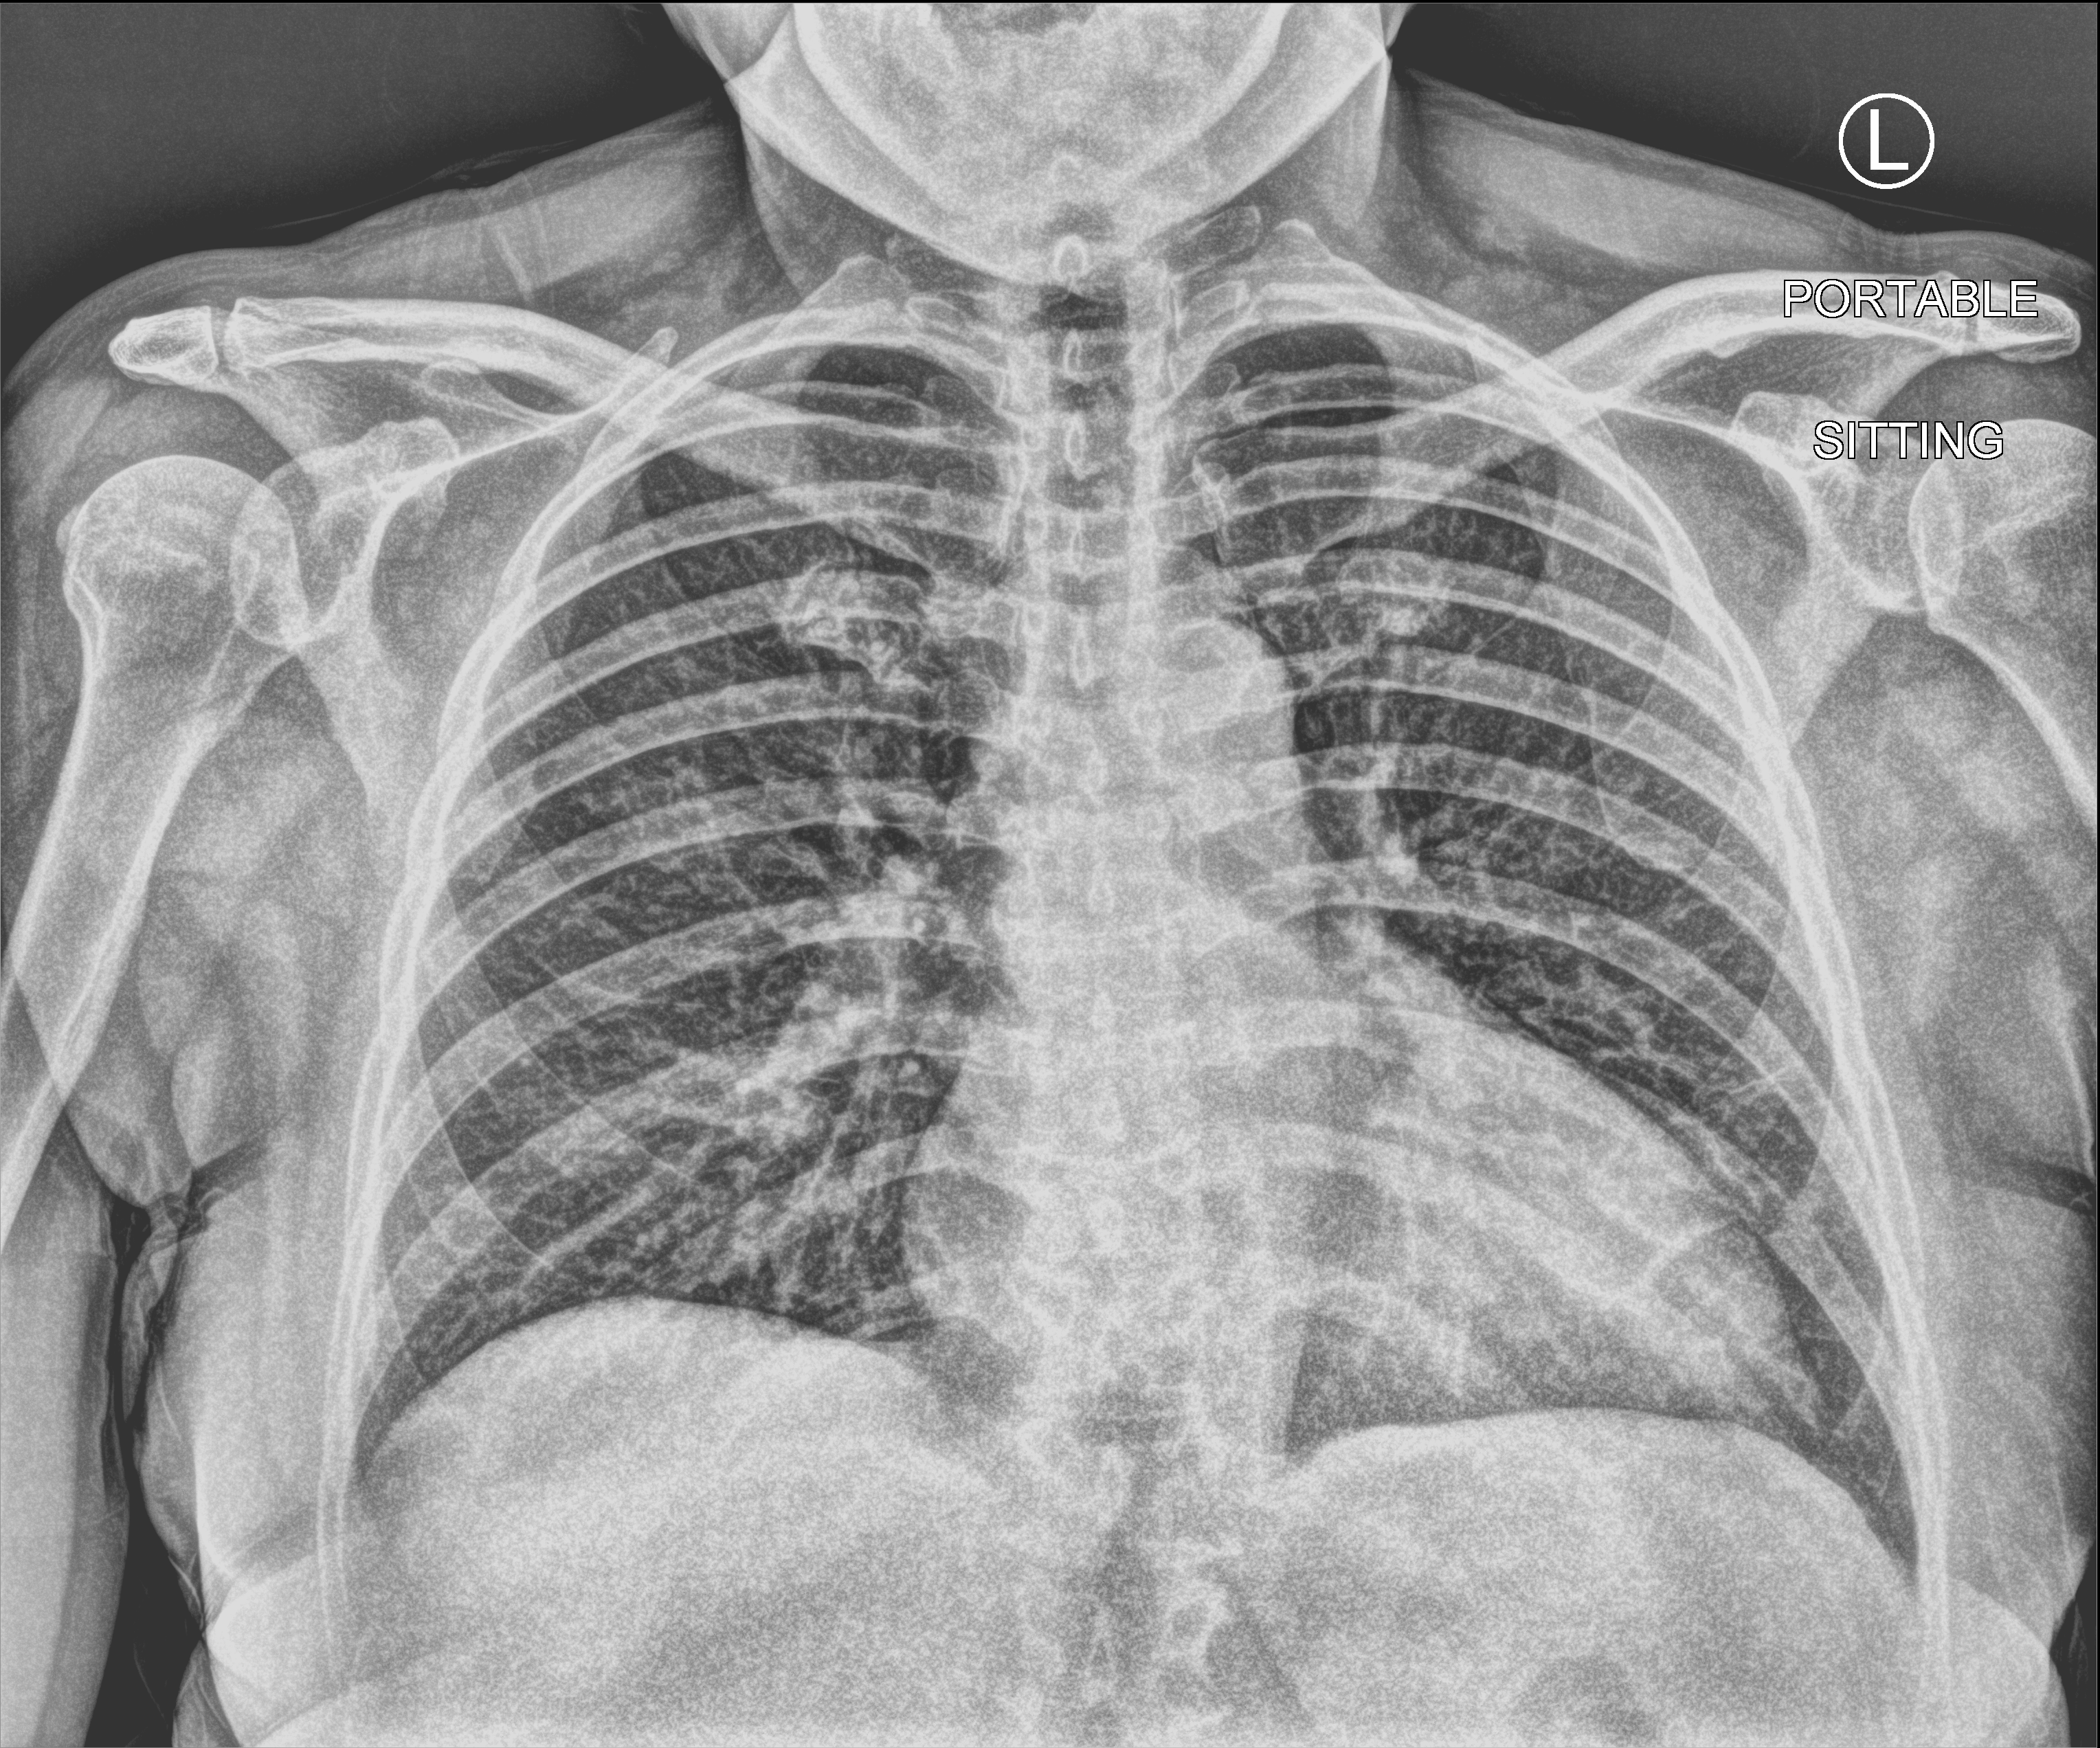
Bedside chest radiograph (computed radiography), anteroposterior (AP) projection. Patient hospitalised with COVID-19; female, aged 60–74 years.
Admission-level facts for this patient (not findings on this image; timing relative to this image not recorded): length of hospital stay: 1 day; mechanically ventilated during this hospital stay: no; admitted to intensive care during this hospital stay: no.